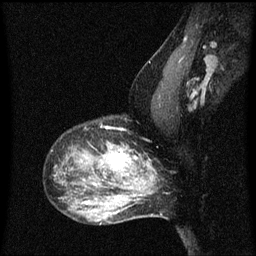
Breast MRI (dynamic contrast-enhanced), one sagittal slice; position 43 of 60 along the scan axis; dynamic contrast-enhanced series, image 2 of 3 at this slice position (ordered by acquisition); 1.5 T; TE 4.2 ms, TR 8 ms; 2 mm slice thickness; 256 × 256 image matrix. Female patient, age 50 years.
Outlined on this slice (semi-automatically segmented with operator editing):
- analysis volume of interest (the breast-tissue region the enhancement analysis was run in; not a lesion): bounding box (x1, y1, x2, y2) in pixels: (91, 144, 141, 189)
- tumour enhancement mask (voxels above the 70 % enhancement threshold inside the analysis volume of interest): (109, 146, 137, 177)